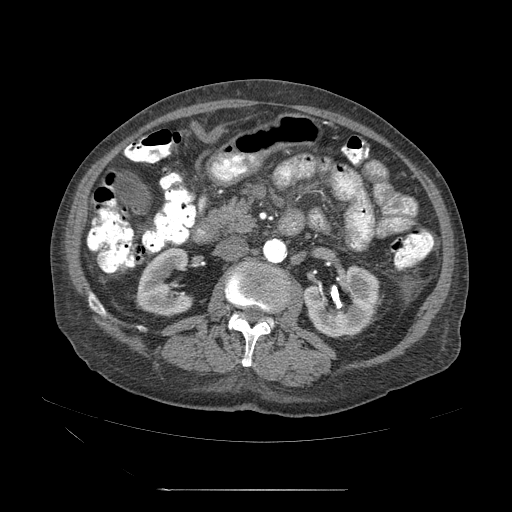
Contrast-enhanced abdominal CT (liver protocol), one axial slice; slice 7 of 71 in the series (ordered by position); 120 kVp; soft-tissue window (W 400 / L 40 HU); 2.5 mm slice thickness; 512 × 512 image matrix, field of view 440 × 440 mm. From the clinical record (not read from this slice): diagnosis: hepatocellular carcinoma (patient treated with transarterial chemoembolisation; whether this scan precedes or follows treatment is not stated here); TNM stage (as recorded): Stage-II; Child-Pugh class: A; tumour nodularity: multinodular.
Outlined on this slice (semi-automatic segmentation, software-assisted and operator-edited):
- abdominal aorta: bounding box <264,239,286,264> (left, top, right, bottom; pixels)